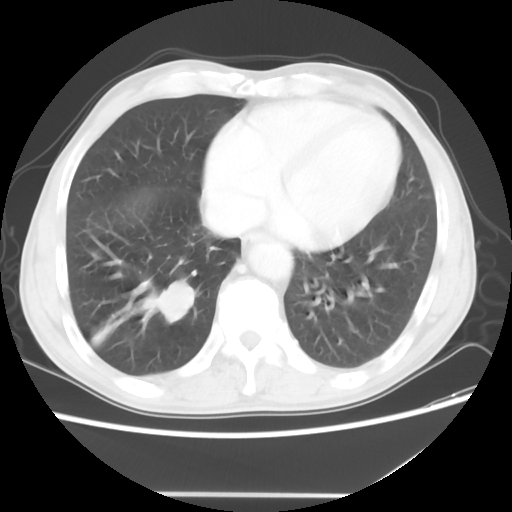
Chest CT, one axial slice; slice 16 of 56 in the series (ordered by position); reconstruction kernel STANDARD; 120 kVp; lung window (W 1500 / L -600 HU); 5 mm slice thickness; 512 × 512 image matrix, field of view 344 × 344 mm. Male patient, age 65 years. Case-level facts recorded for this patient, not image findings: clinical TNM (as recorded): T1c N3 M0; histopathological grade: G3.
Annotated regions visible in this slice (bounding box drawn by a radiologist):
- lung tumour (recorded histology: small cell carcinoma): box from (x=140, y=281) to (x=201, y=324) px